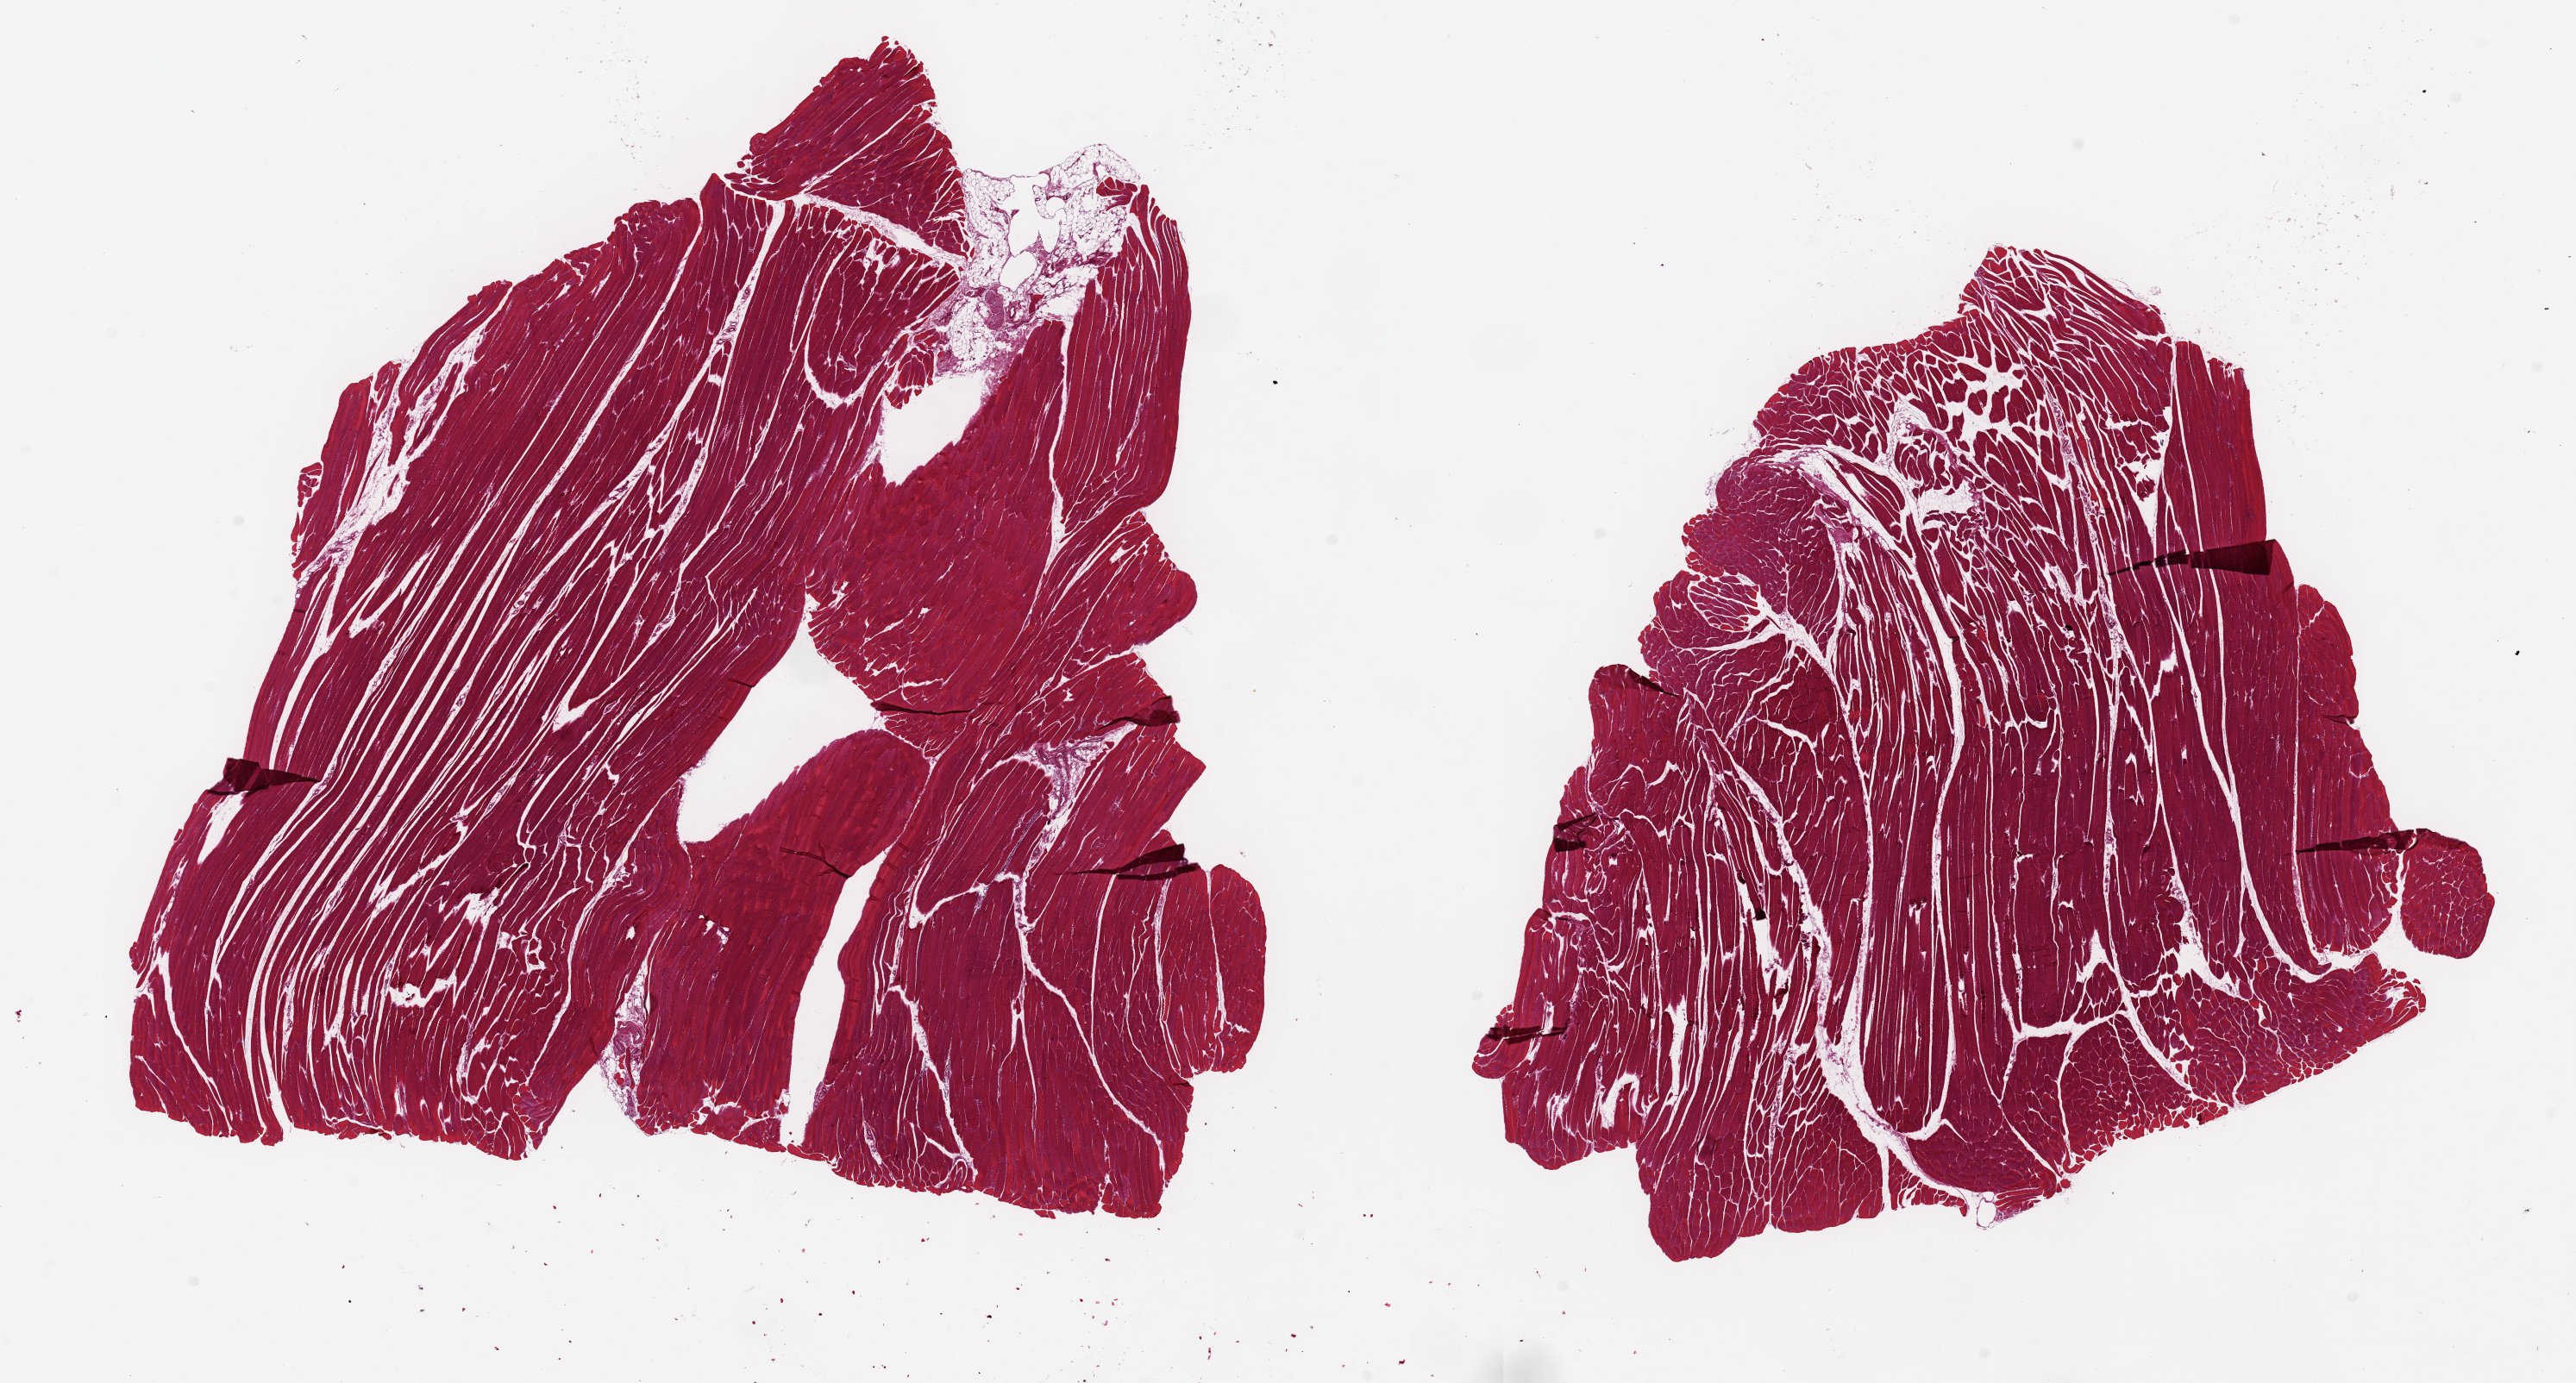
Haematoxylin and eosin whole-slide image, a low-resolution overview of the entire scanned area, about 23.6 x 12.7 mm (slide scanned at 20x). PAXgene-fixed paraffin-embedded (PFPE) section. Section of skeletal muscle (target tissue). Tissue donor sample. Female donor.
• reviewer comment on this tissue sample: 2 pieces, ~9x9mm, minmal interstital fat